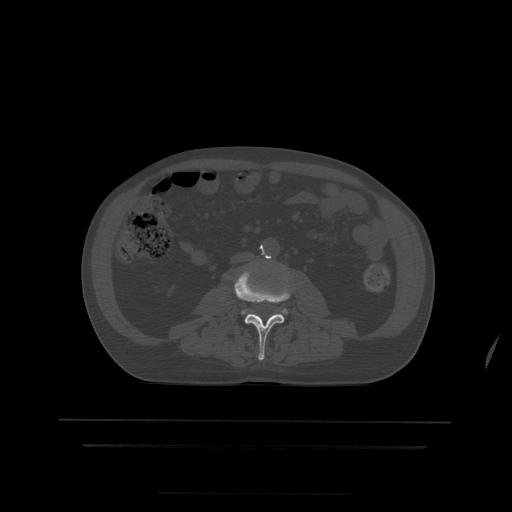
CT including the spine, one axial slice; bone window (W 1800 / L 400 HU); 512 × 512 image matrix, field of view 436 × 436 mm. Patient age 68 years. From the clinical record (not read from this slice): primary cancer: urothelial.
Structures marked on this image (semi-automatically segmented with operator editing):
- L3 vertebra: bounding box (x1, y1, x2, y2) in pixels: (234, 269, 292, 361)
- L4 vertebra: (243, 310, 288, 314)